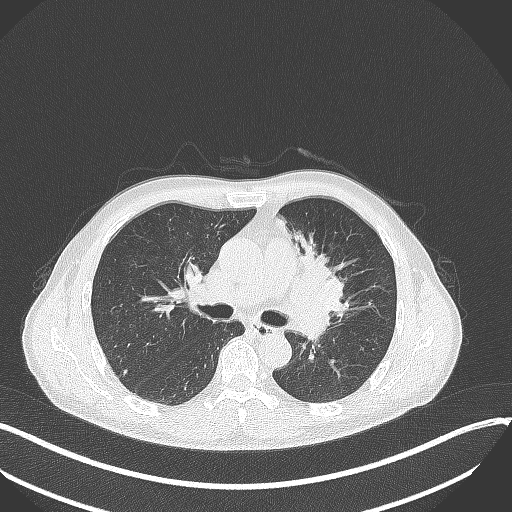
Chest CT, one axial slice. Reconstruction kernel B70f. 120 kVp. Lung window (W 1500 / L -600 HU). 1 mm slice thickness. 512 × 512 image matrix, field of view 400 × 400 mm. Patient: male, 56 years. Case-level facts recorded for this patient, not image findings: clinical TNM (as recorded): T2a N0 M0.
Structures marked on this image (rectangle marked by the reading radiologist):
- lung tumour (recorded histology: squamous cell carcinoma): box from (x=287, y=250) to (x=350, y=315) px